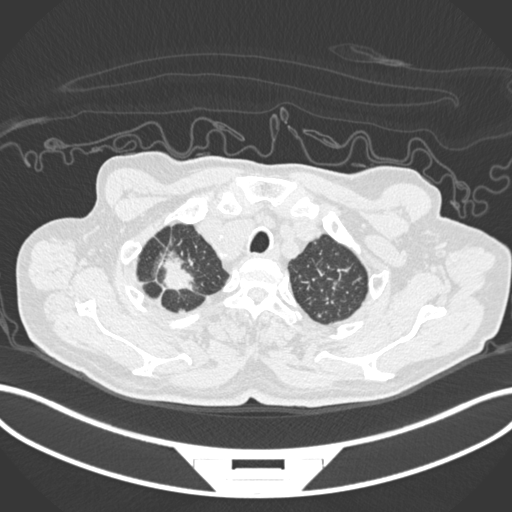
Chest CT, one axial slice. Reconstruction kernel B30f. 120 kVp. Lung window (W 1500 / L -600 HU). 512 × 512 image matrix, field of view 400 × 400 mm. Male patient, age 69 years. From the clinical record (not read from this slice): clinical TNM (as recorded): T1c N1 M1.
Annotated regions visible in this slice (bounding box drawn by a radiologist):
- lung tumour (recorded histology: adenocarcinoma): box from (x=151, y=246) to (x=202, y=296) px